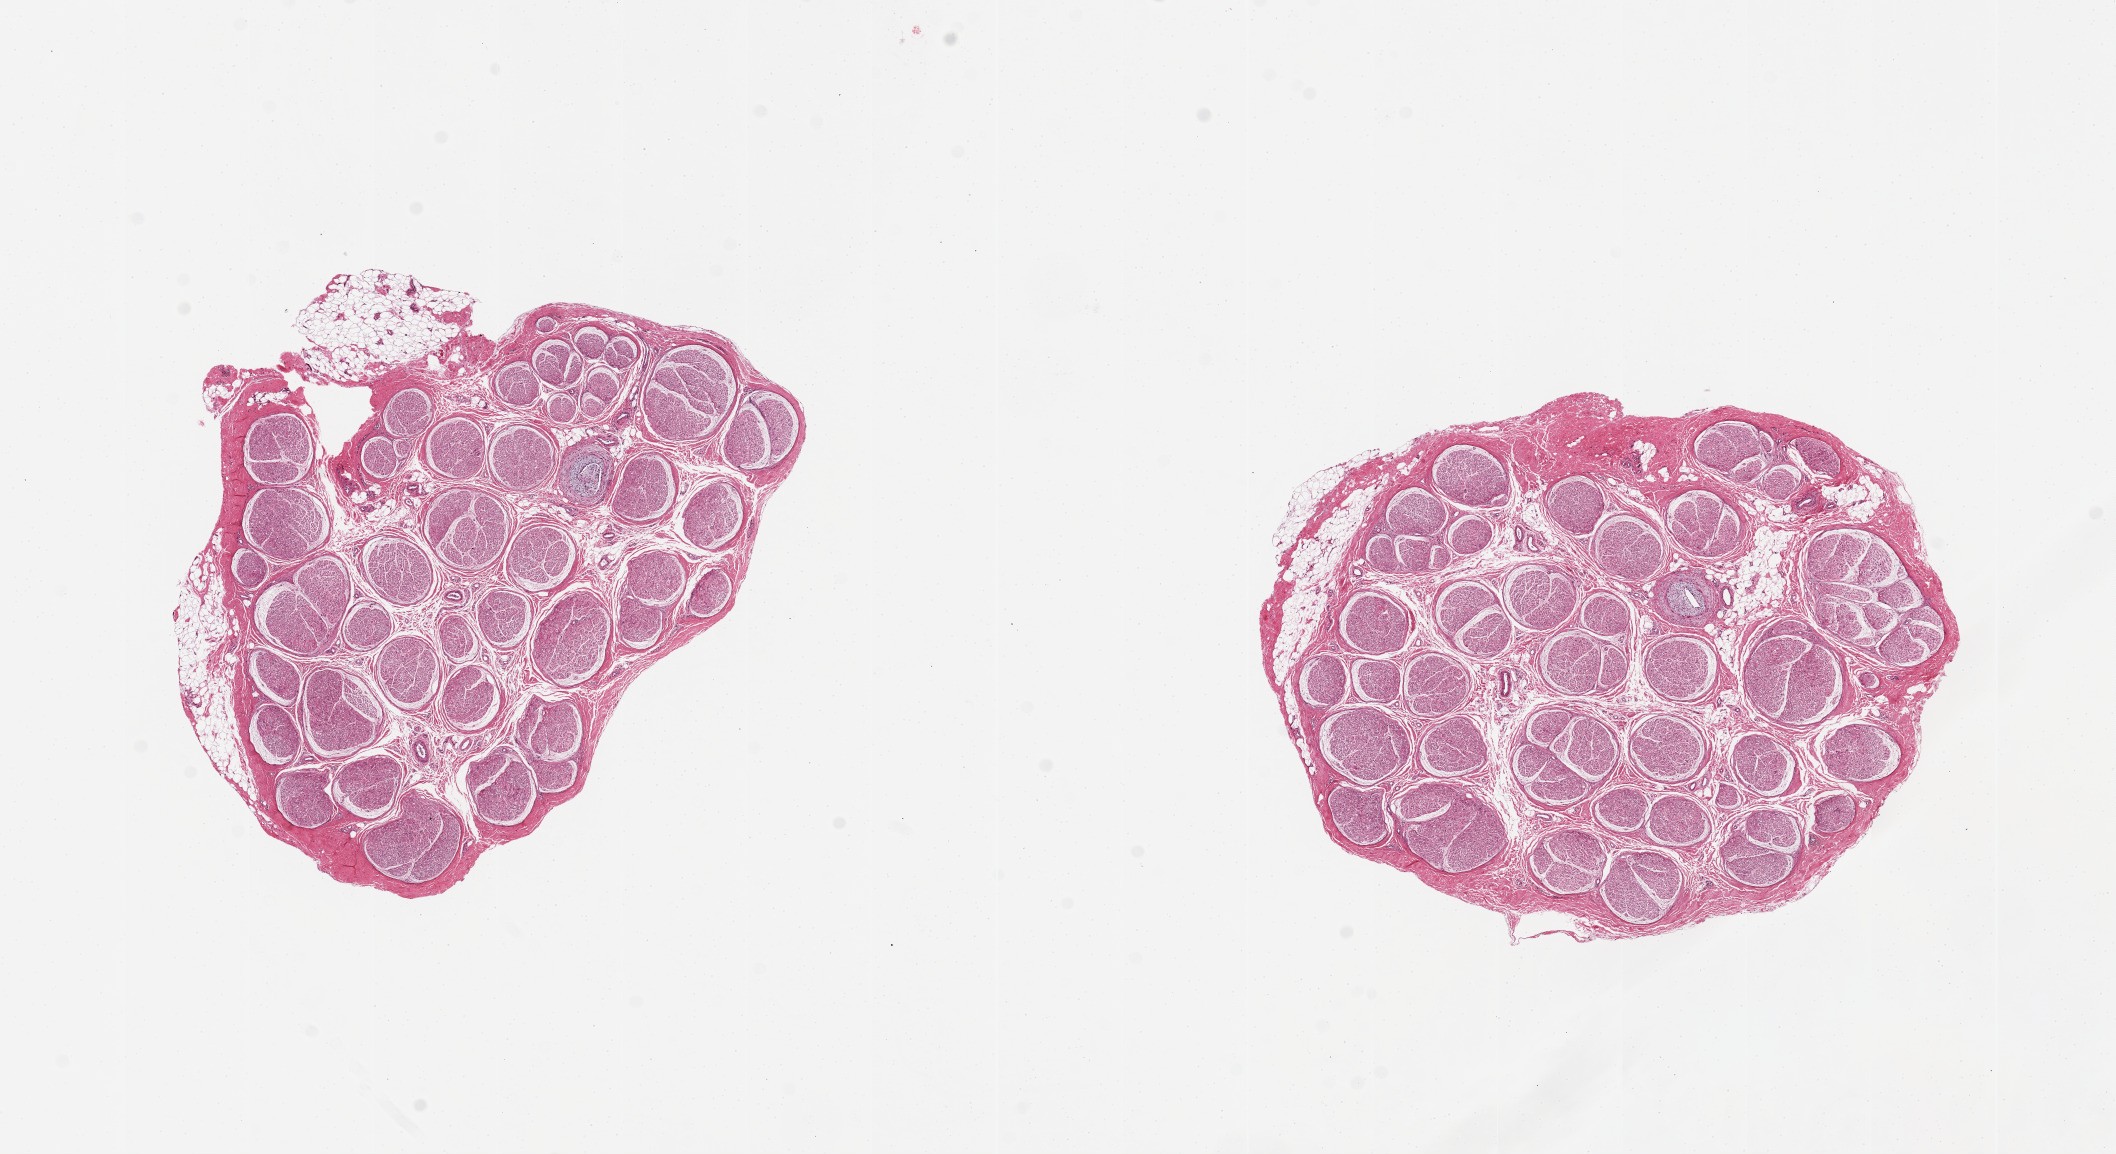
Whole-slide image, H&E stain, whole scanned area (about 16.7 x 9.1 mm) shown as a low-resolution overview; PAXgene-fixed paraffin-embedded (PFPE) section; target tissue: tibial nerve; tissue donor sample. Donor: female.
Reviewer comment on this tissue sample: 2 pieces, 5x4.5 & 5x4mm; minute adherent nubbins of fat on both, ~0.5mm.